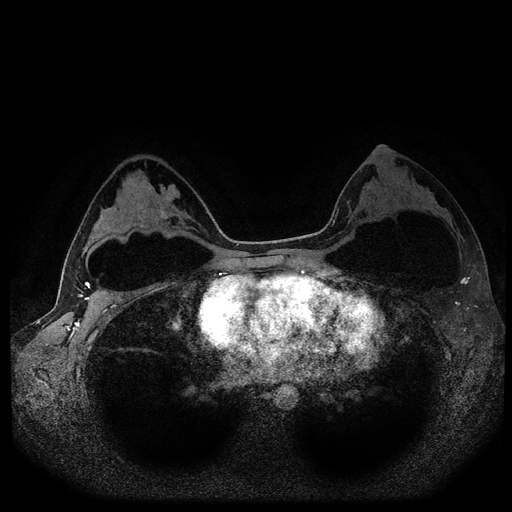
Breast MRI (dynamic contrast-enhanced, multi-phase), one axial slice. Position 64 of 116 along the scan axis. Dynamic contrast-enhanced series, time point 2 of 5 at this slice position (early post-contrast). 1.5 T. TE 2.6 ms, TR 5.4 ms. 2 mm slice thickness. 512 × 512 image matrix, field of view 340 × 340 mm. Patient: female, 33 years.
Structures marked on this image (semi-automatically segmented with operator editing):
- breast lesion (labelled benign in the annotation): bounding box (x1, y1, x2, y2) in pixels: (158, 183, 180, 219)